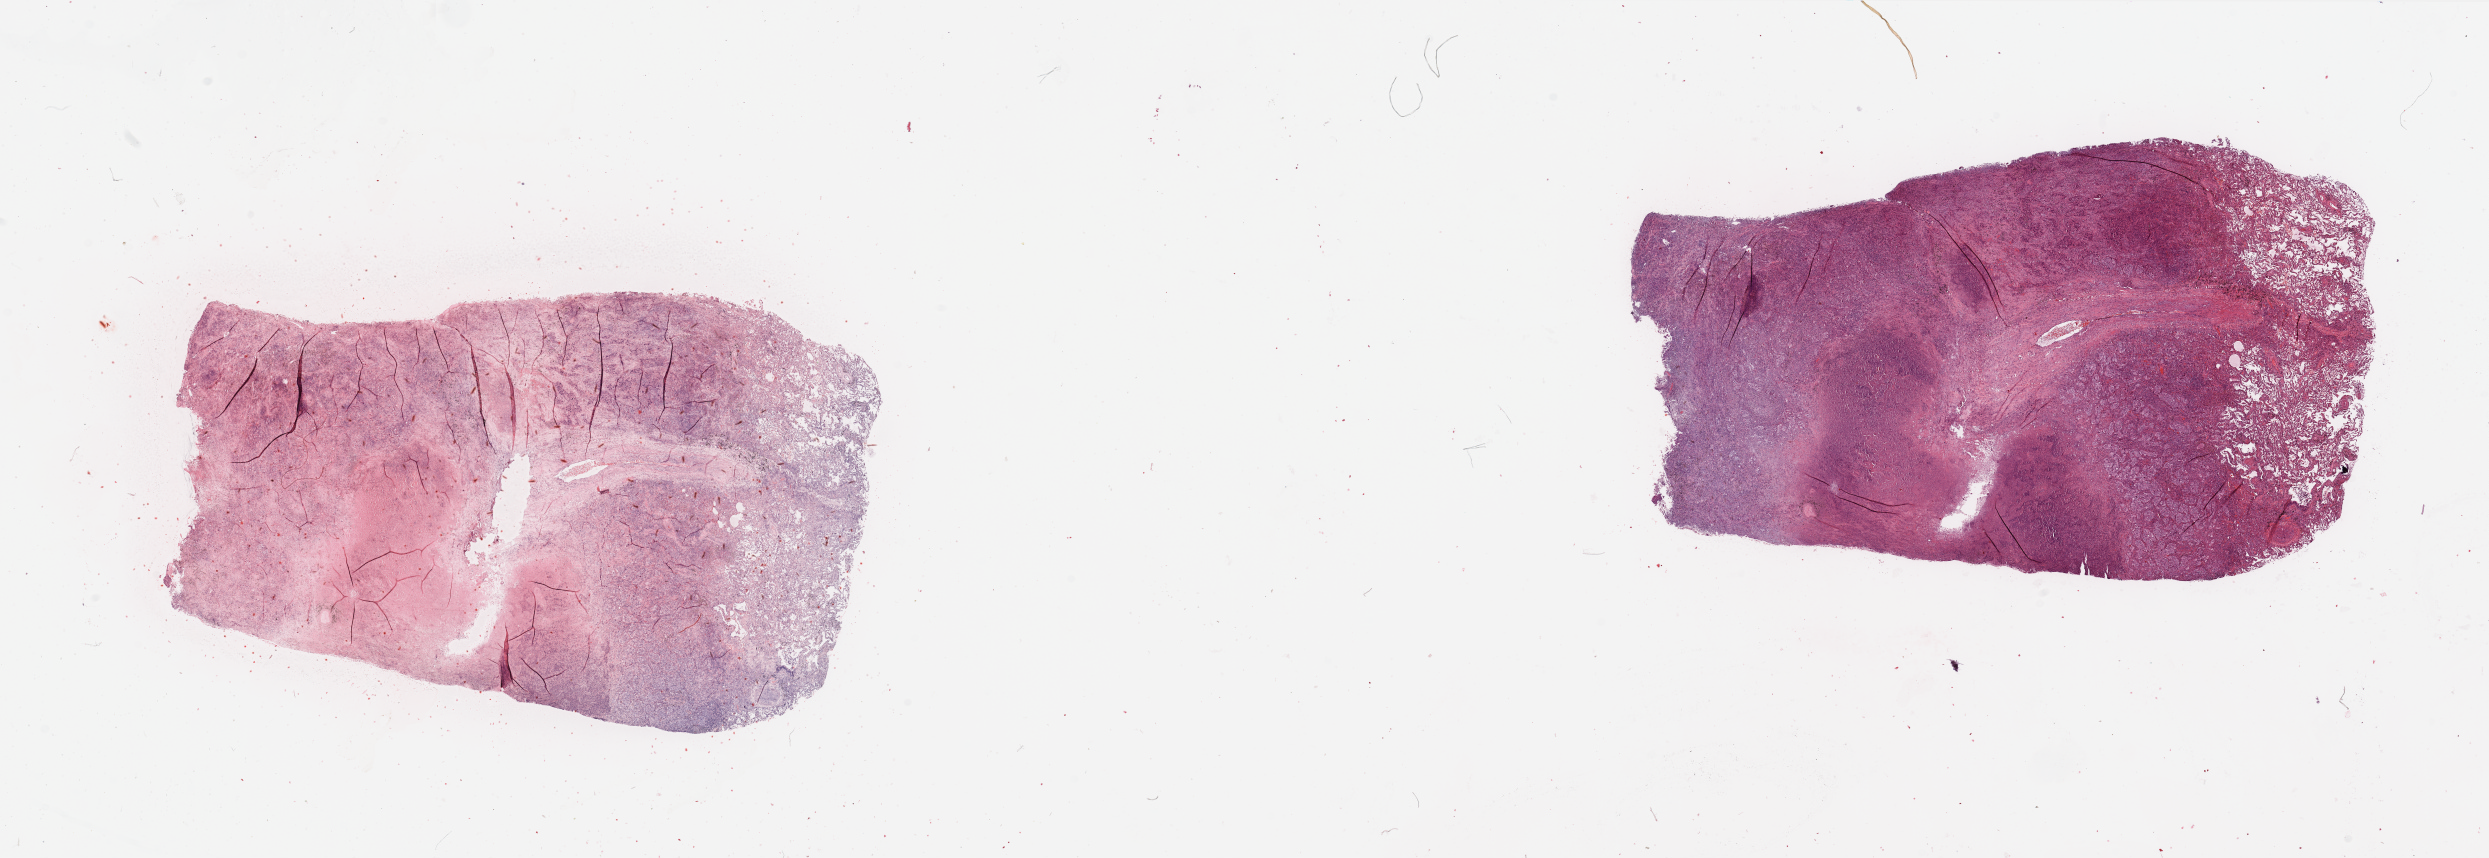
H&E whole-slide image — a low-resolution overview of the entire scanned area, about 39.4 x 13.6 mm (acquisition: 20x scan), tumour tissue sample, lung. 65-year-old male patient. Histologic grade: G3 (poorly differentiated).
AJCC pathologic stage: IIIA. Histologic diagnosis: Adenocarcinoma, NOS.